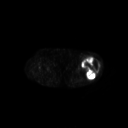
FDG PET of an extremity soft-tissue mass (from a PET/CT study), one axial slice. Slice 224 of 267 in the series (ordered by position). 3.27 mm slice thickness. 128 × 128 image matrix, field of view 700 × 700 mm. Female patient, age 62 years. From the clinical record (not read from this slice): histological type: undifferentiated – high grade; grade: high; site of the primary tumour: left thigh.
Outlined on this slice (expert contour drawn on MRI and transferred to this co-registered scan by the dataset authors):
- gross tumour volume including surrounding oedema: bounding box [x1, y1, x2, y2] px = [81, 56, 100, 79]
- gross tumour volume (mass): [81, 56, 99, 79]